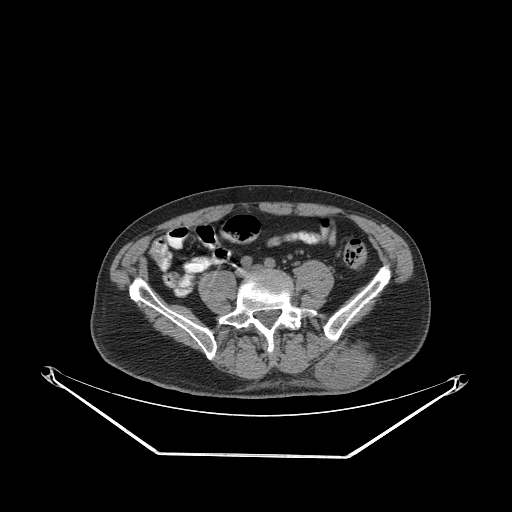
CT of an extremity soft-tissue mass (from a PET/CT study), one axial slice; slice 89 of 267 in the series (ordered by position); soft-tissue window (W 400 / L 40 HU); 3.75 mm slice thickness; 512 × 512 image matrix, field of view 500 × 500 mm. Male patient. From the clinical record (not read from this slice): histological type: leiomyosarcoma; grade: intermediate; site of the primary tumour: left pelvis.
Structures marked on this image (expert contour drawn on MRI and transferred to this co-registered scan by the dataset authors):
- gross tumour volume (mass): bounding box (x1, y1, x2, y2) in pixels: (315, 342, 376, 389)